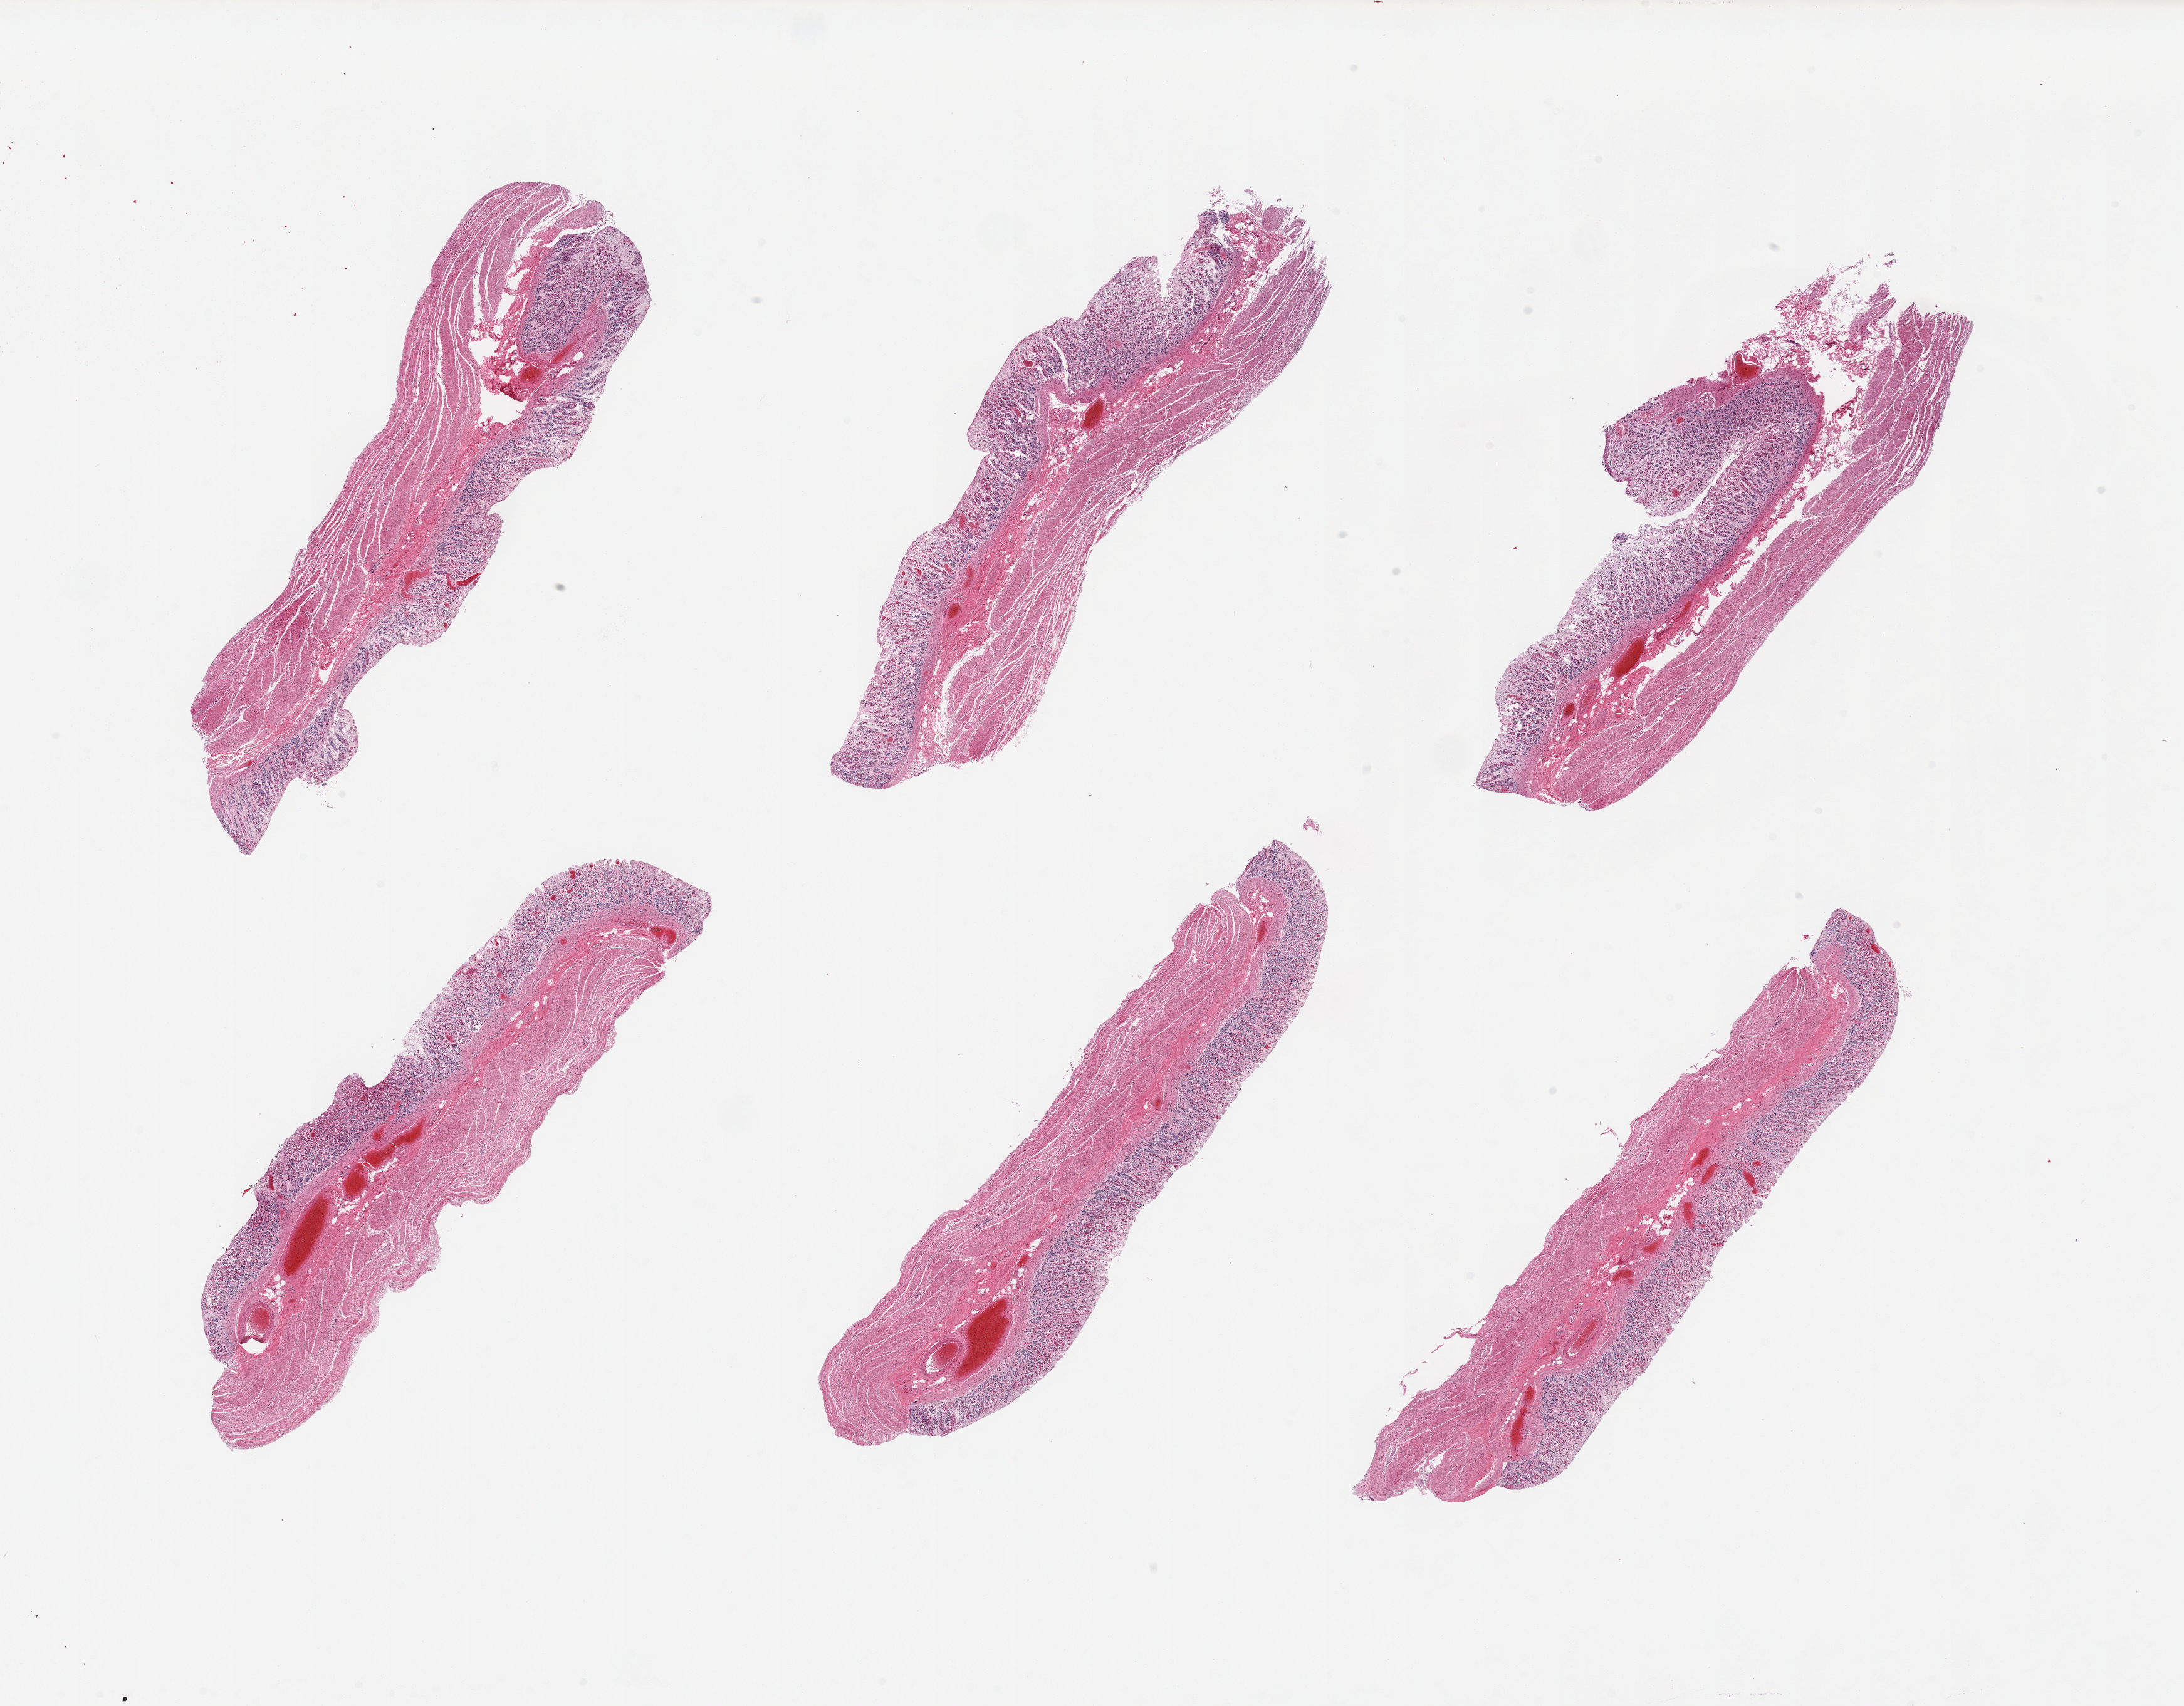
Hematoxylin and eosin (H&E) whole-slide image, brightfield, low-resolution overview of the scanned area, about 27.6 x 21.5 mm (from a 20x scan); PAXgene-fixed paraffin-embedded (PFPE) section; section of stomach (target tissue); donor tissue sample. Male donor.
• reviewer comment on this tissue sample: 6 pieces; mucosa more autolyzed than muscle